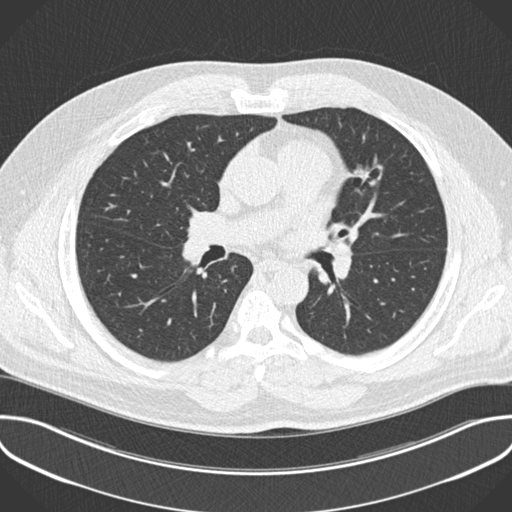
Low-dose screening chest CT, one axial slice; position 122 of 201 along the scan axis; lung window (W 1500 / L -600 HU); 2 mm slice thickness; 512 × 512 image matrix, field of view 386 × 386 mm.
Annotated regions visible in this slice (outlined manually by an expert reader):
- lesion 1 (tumor, upper lobe of left lung): bounding box <356,169,370,178> (left, top, right, bottom; pixels)